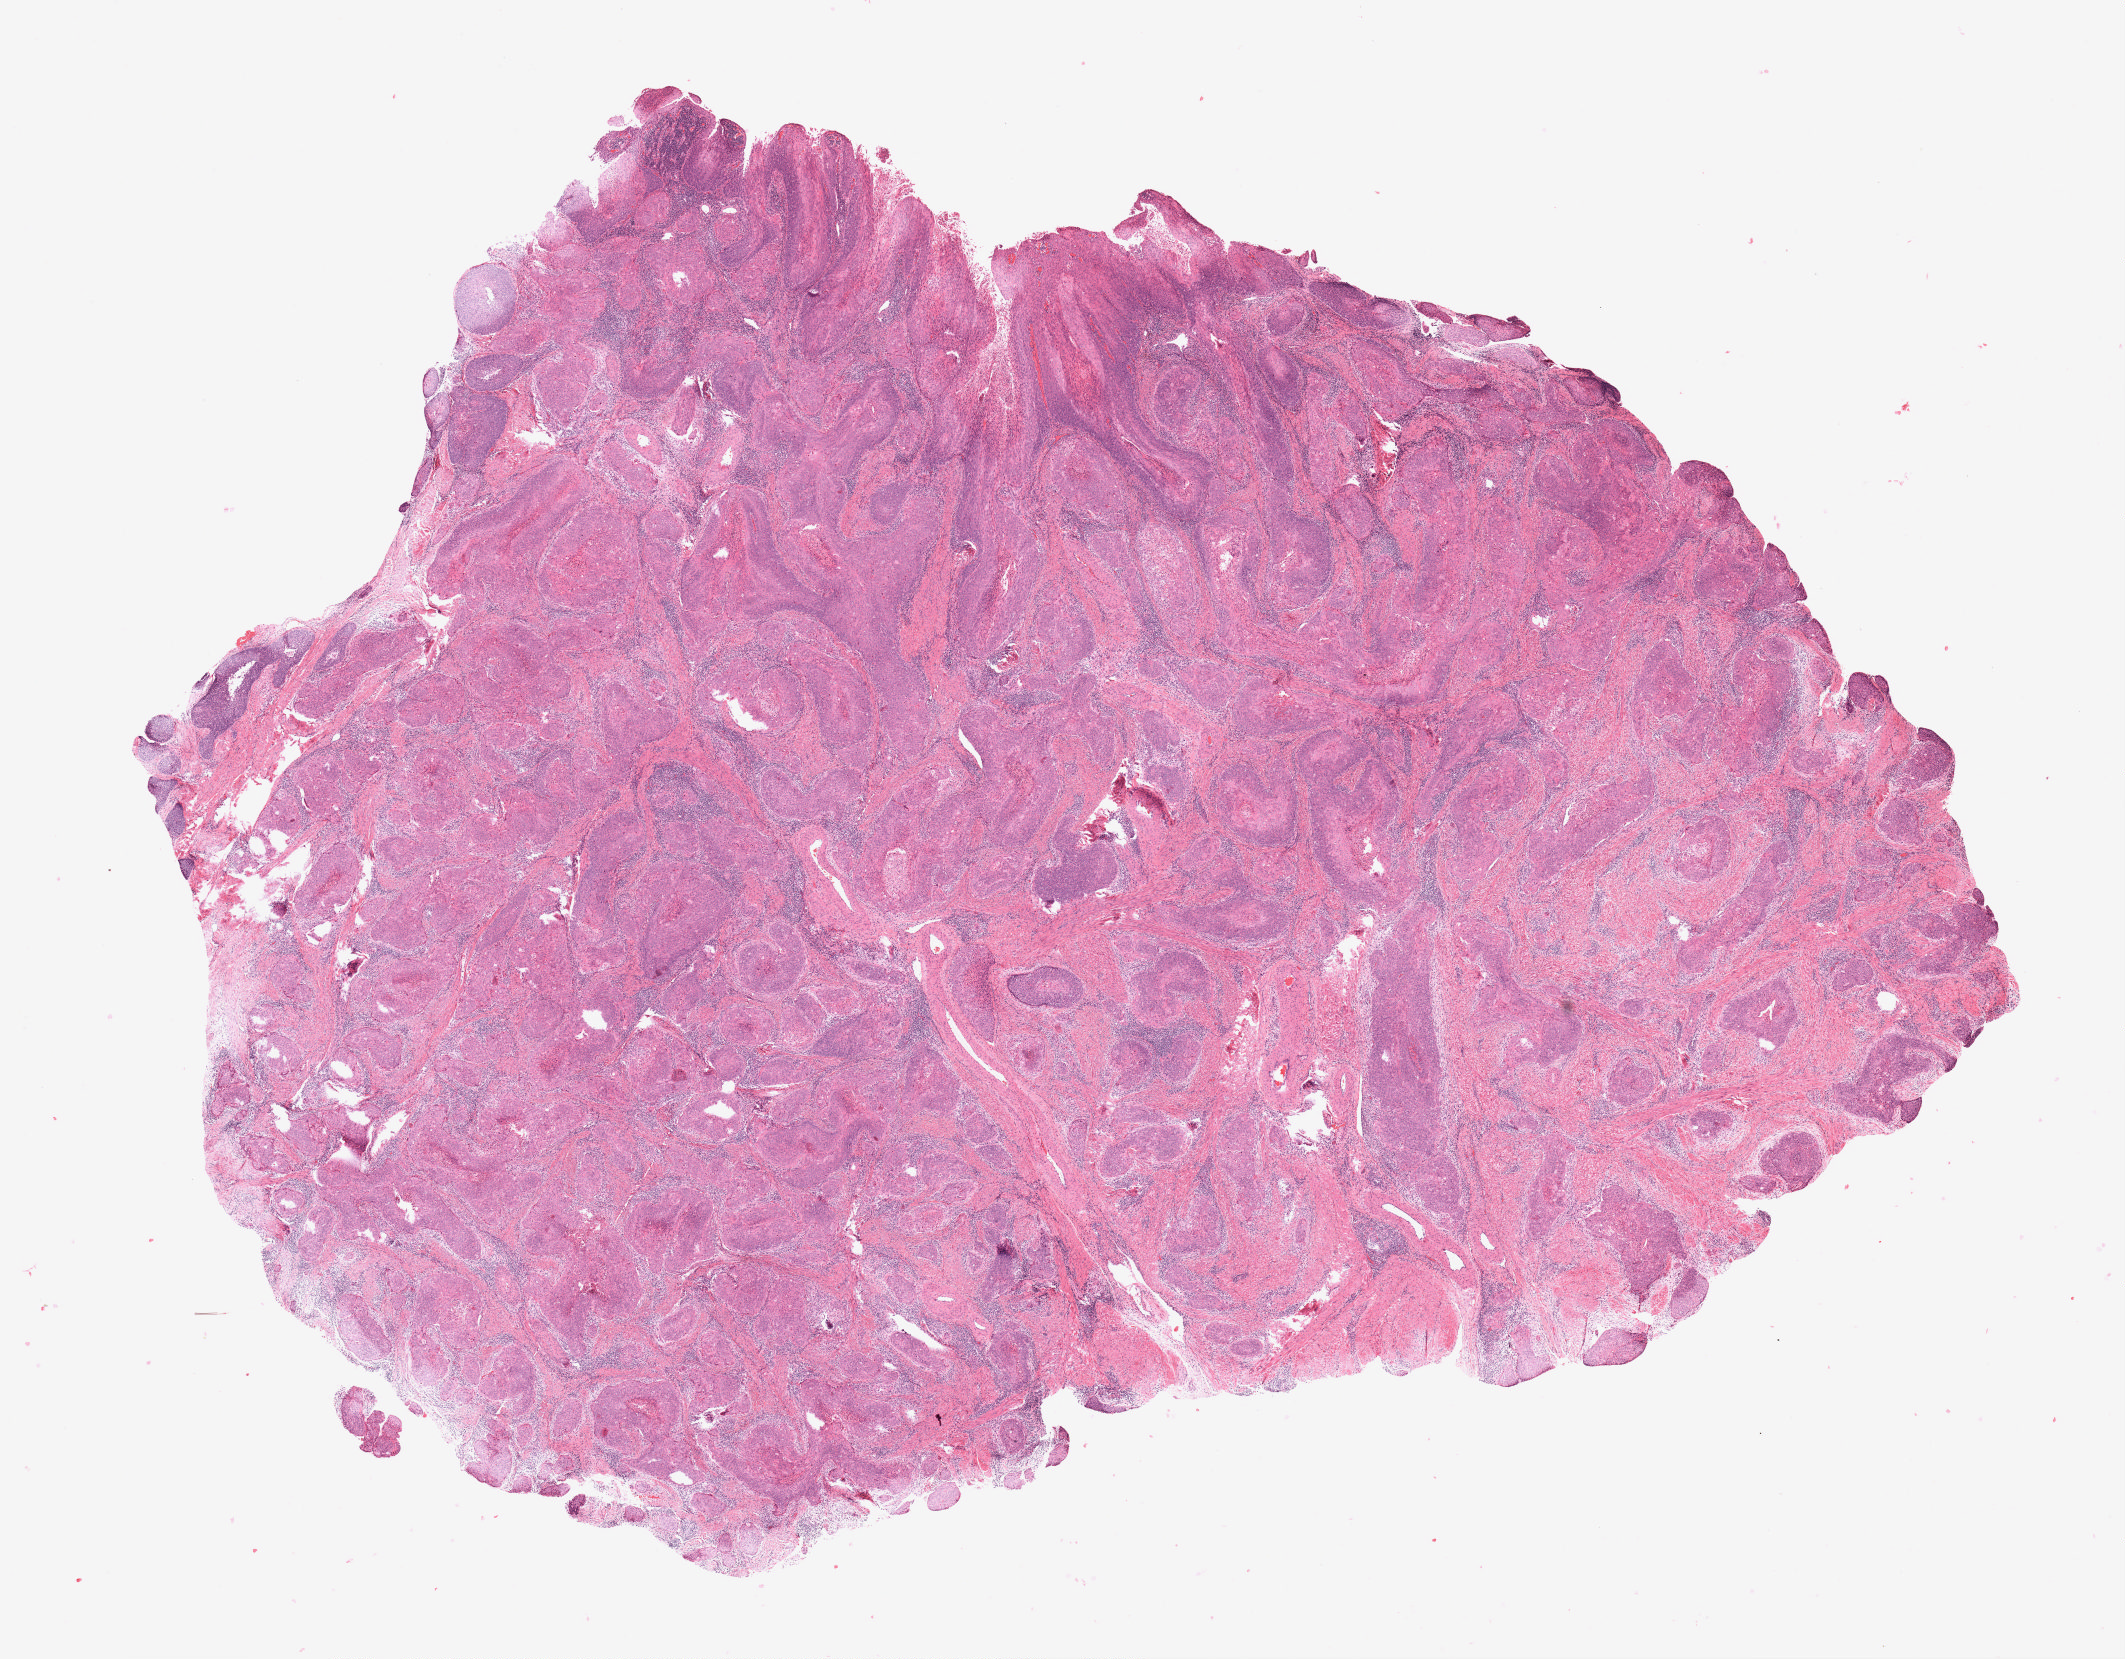
H&E whole-slide image — whole scanned area (about 17.0 x 13.2 mm, acquisition: 20x scan) shown as a low-resolution overview. Formalin-fixed paraffin-embedded (FFPE) diagnostic section. Sample: primary tumour, cervix. Female patient; age at initial diagnosis 27 years. Histologic grade: G2 (moderately differentiated).
• lymph nodes positive (case pathology): 0 of 17 examined
• FIGO stage: IIA1
• pathologic diagnosis: Squamous cell carcinoma, large cell, nonkeratinizing, NOS (cervix uteri)